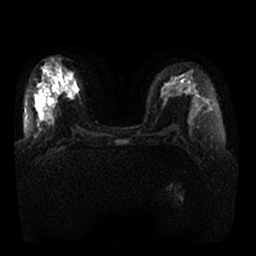
Breast MRI, one axial slice. Position 11 of 25 along the scan axis. Diffusion-weighted series; image 2 of 4 stored at this slice position (different b-values; order by instance number). 1.5 T. 4 mm slice thickness. 256 × 256 image matrix. Female patient.
Annotated regions visible in this slice (expert manual segmentation):
- tumour on diffusion-weighted imaging: bounding box <68,82,77,95> (left, top, right, bottom; pixels)